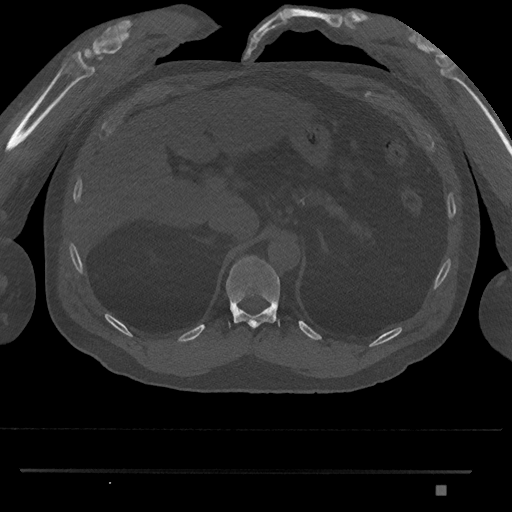
CT including the spine, one axial slice. Position 946 of 1134 along the scan axis. Reconstruction kernel Br40s/3. Bone window (W 1800 / L 400 HU). 512 × 512 image matrix, field of view 429 × 429 mm. Patient: male, 65 years. Case-level facts recorded for this patient, not image findings: primary cancer: prostate.
Annotated regions visible in this slice (semi-automatically segmented with operator editing):
- T11 vertebra: bounding box (x1, y1, x2, y2) in pixels: (226, 255, 280, 329)